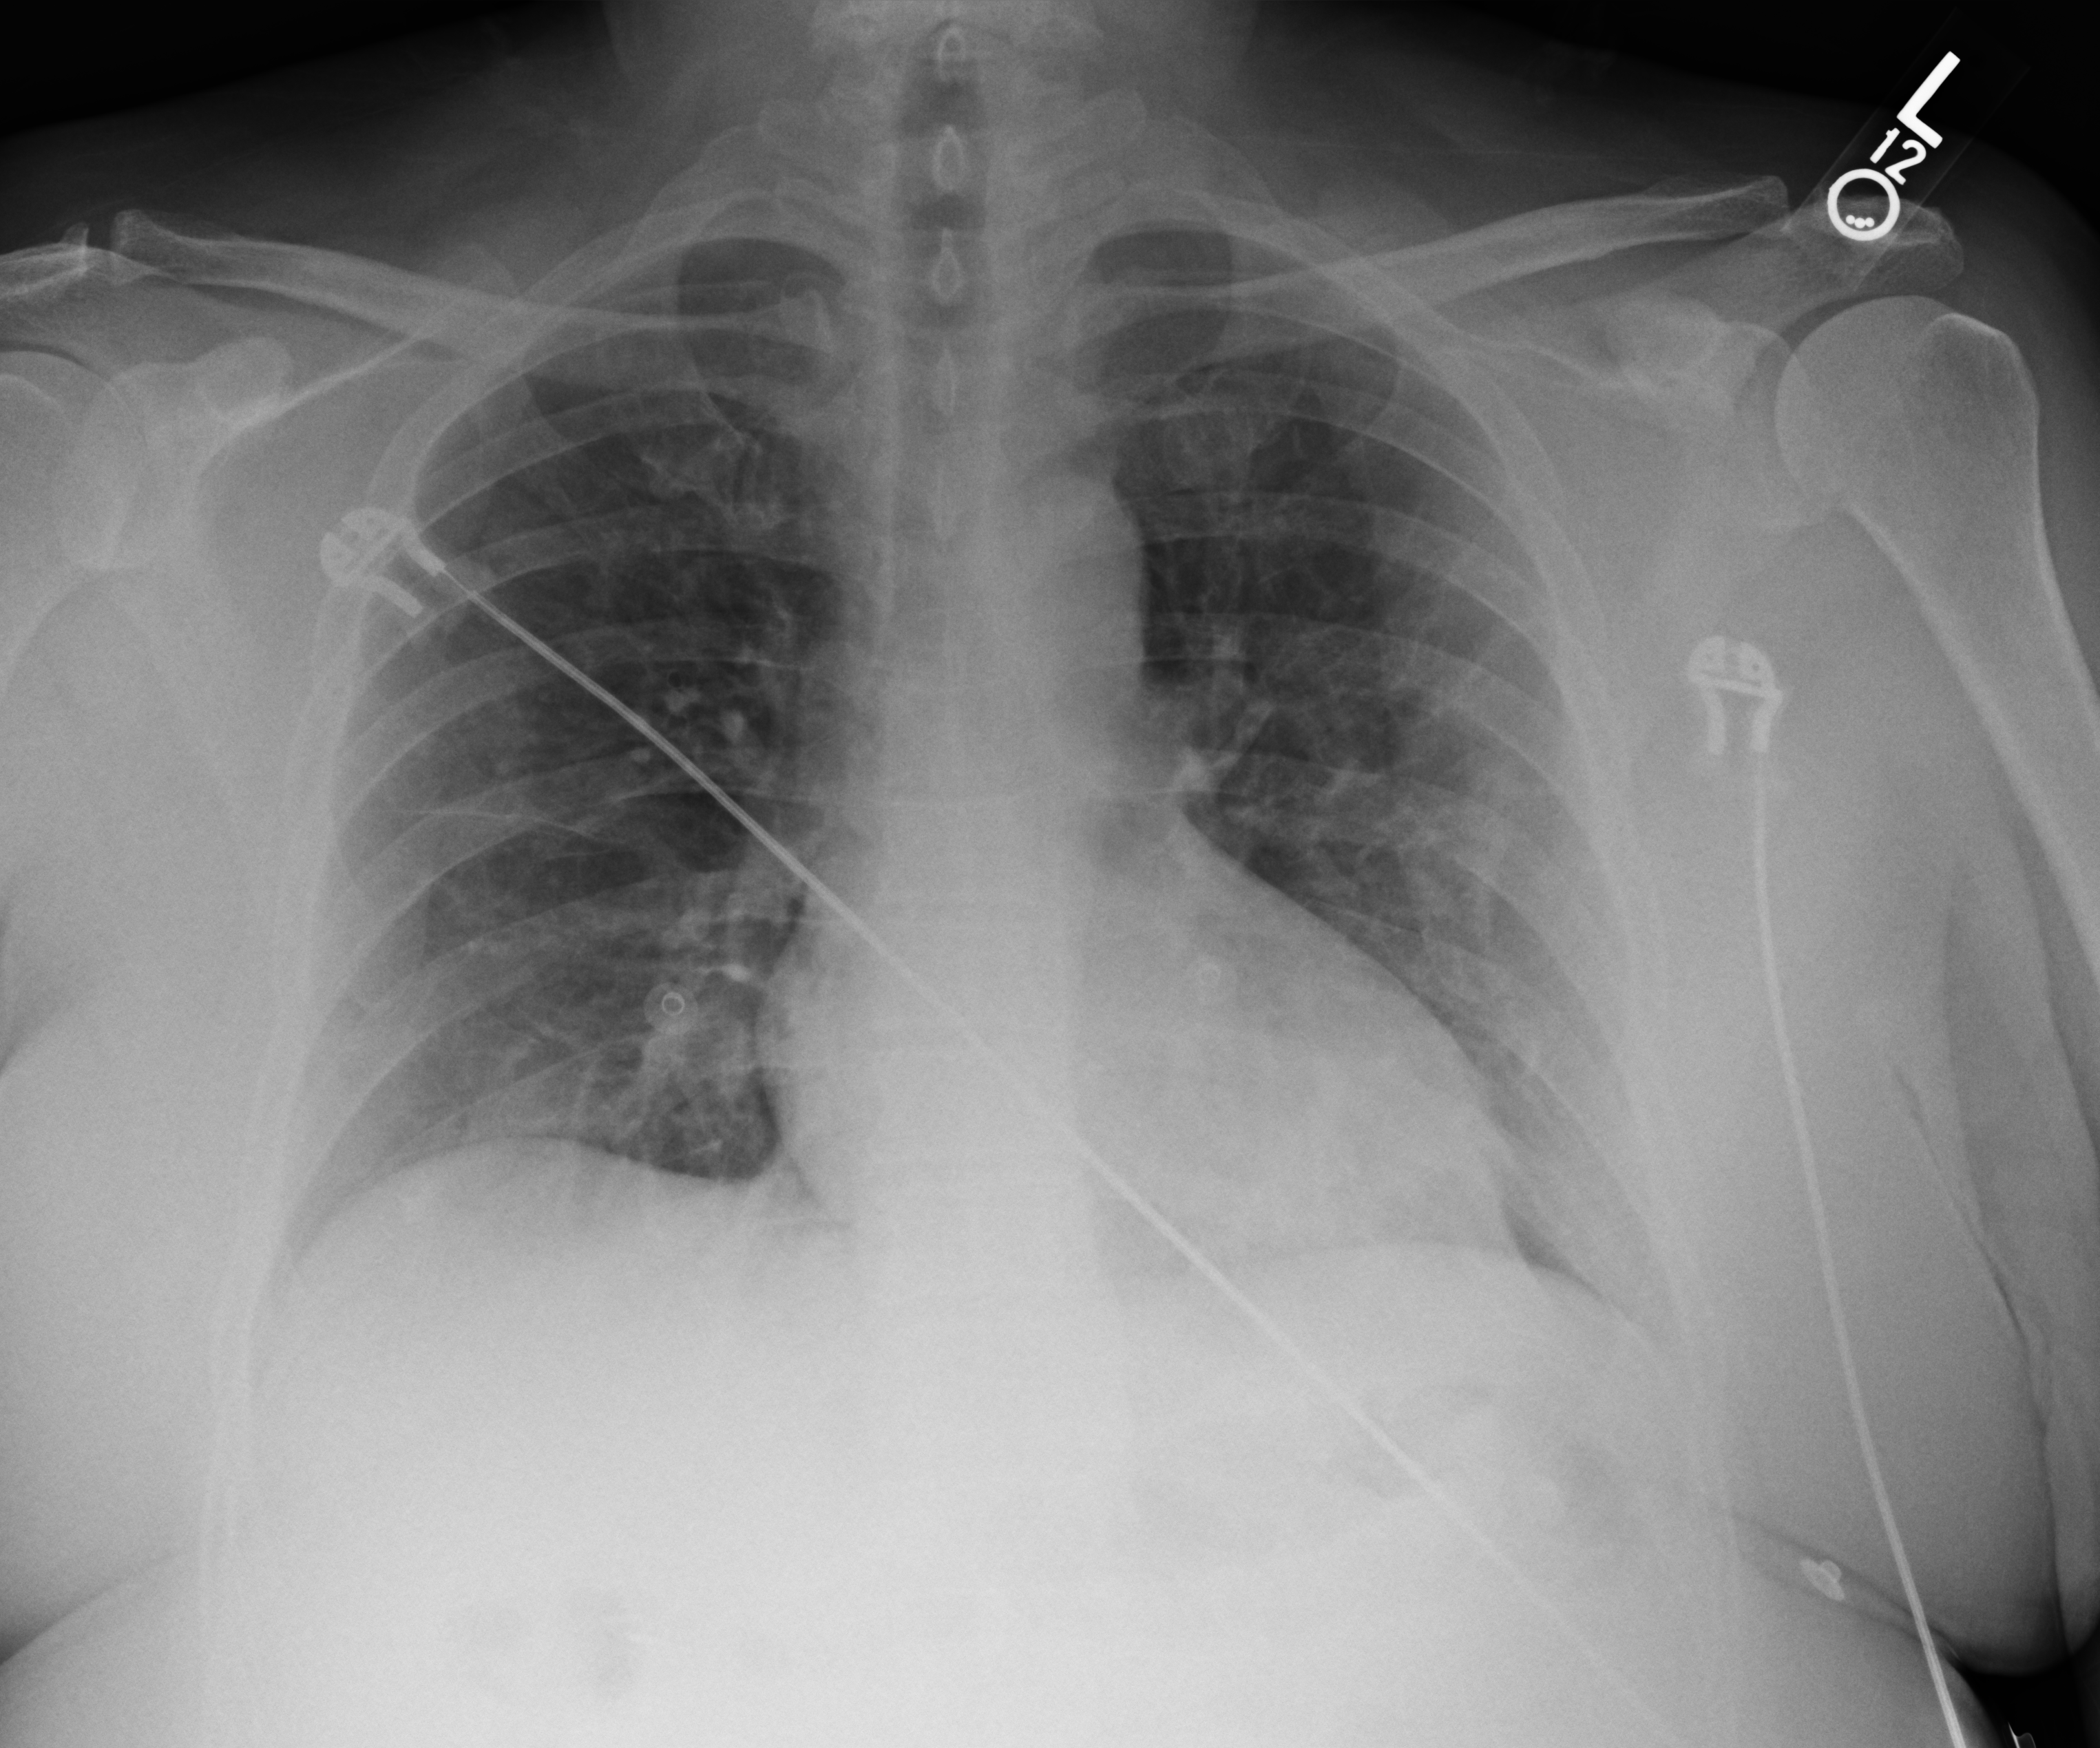
Portable chest radiograph; anteroposterior (AP) projection. Patient hospitalised with COVID-19; male, aged 60–74 years.
From the hospital-stay record, not from the radiograph (when in the stay this image was taken is not recorded): length of hospital stay: 4 days; mechanically ventilated during this hospital stay: no; chronic kidney disease (admission record): no.